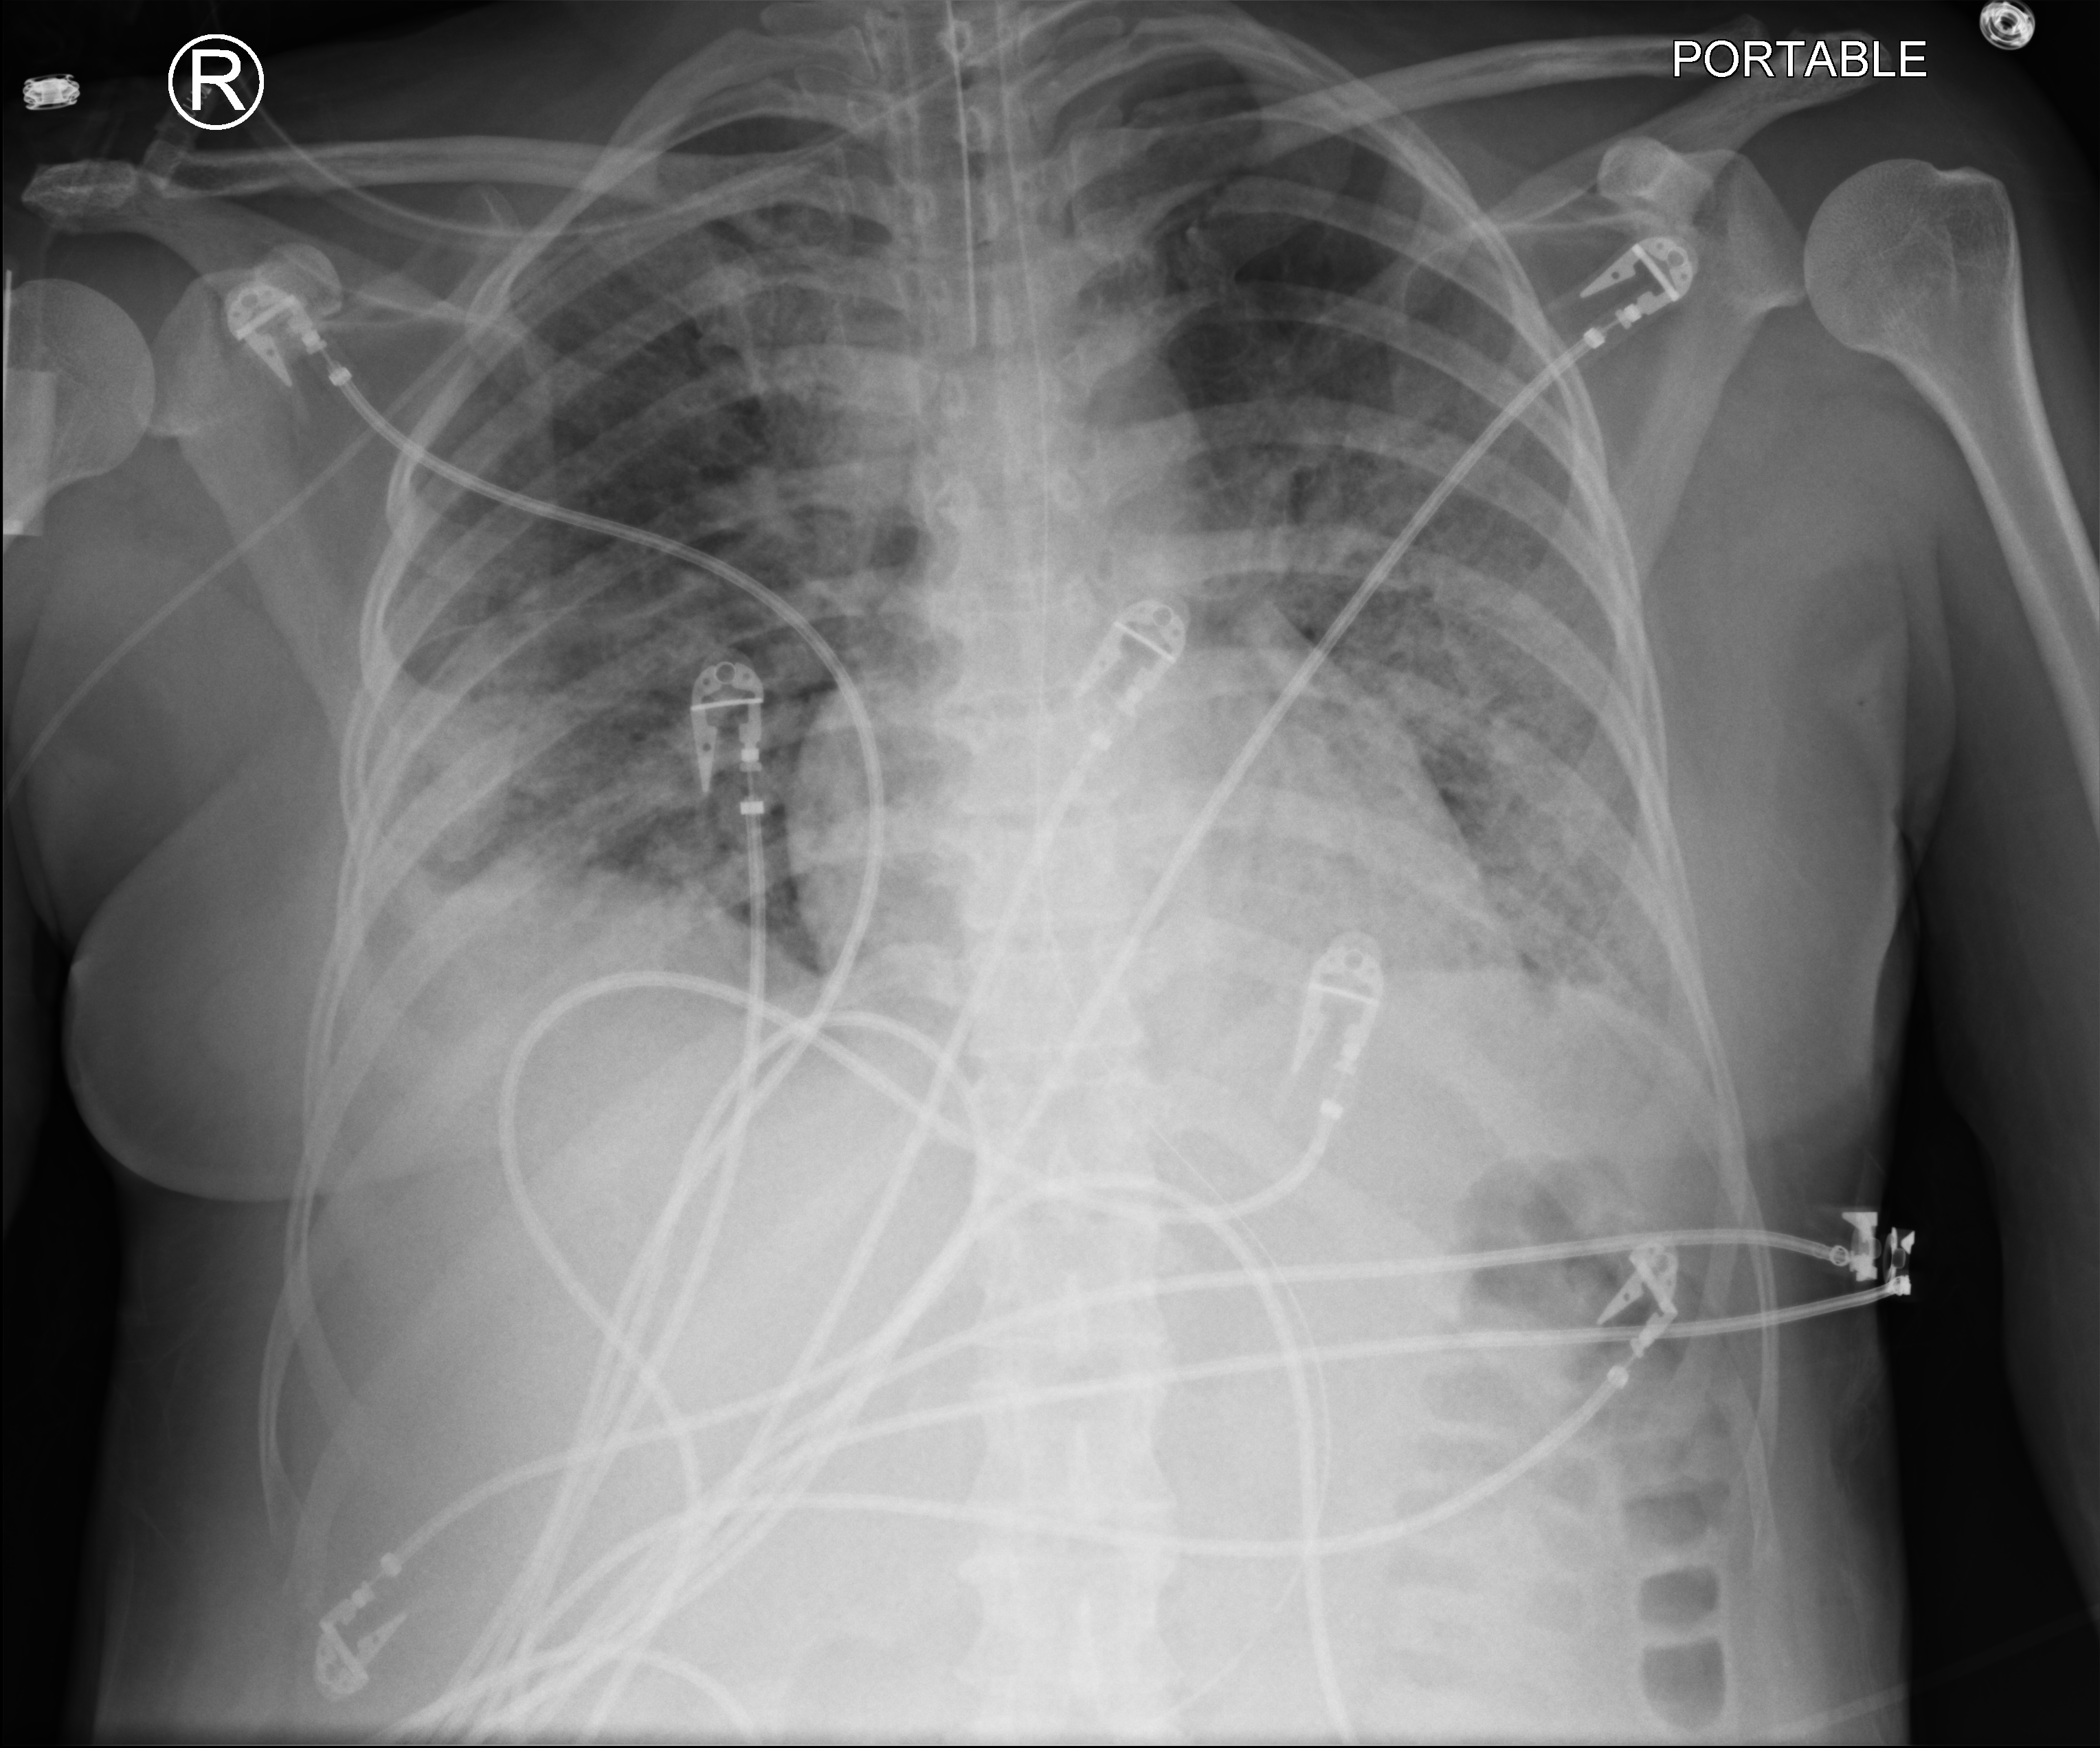
Bedside chest radiograph (computed radiography), anteroposterior (AP) projection. Female patient hospitalised with COVID-19, age 18–59 years.
From the hospital-stay record, not from the radiograph (when in the stay this image was taken is not recorded): mechanically ventilated during this hospital stay: yes; other chronic lung disease (admission record): no.